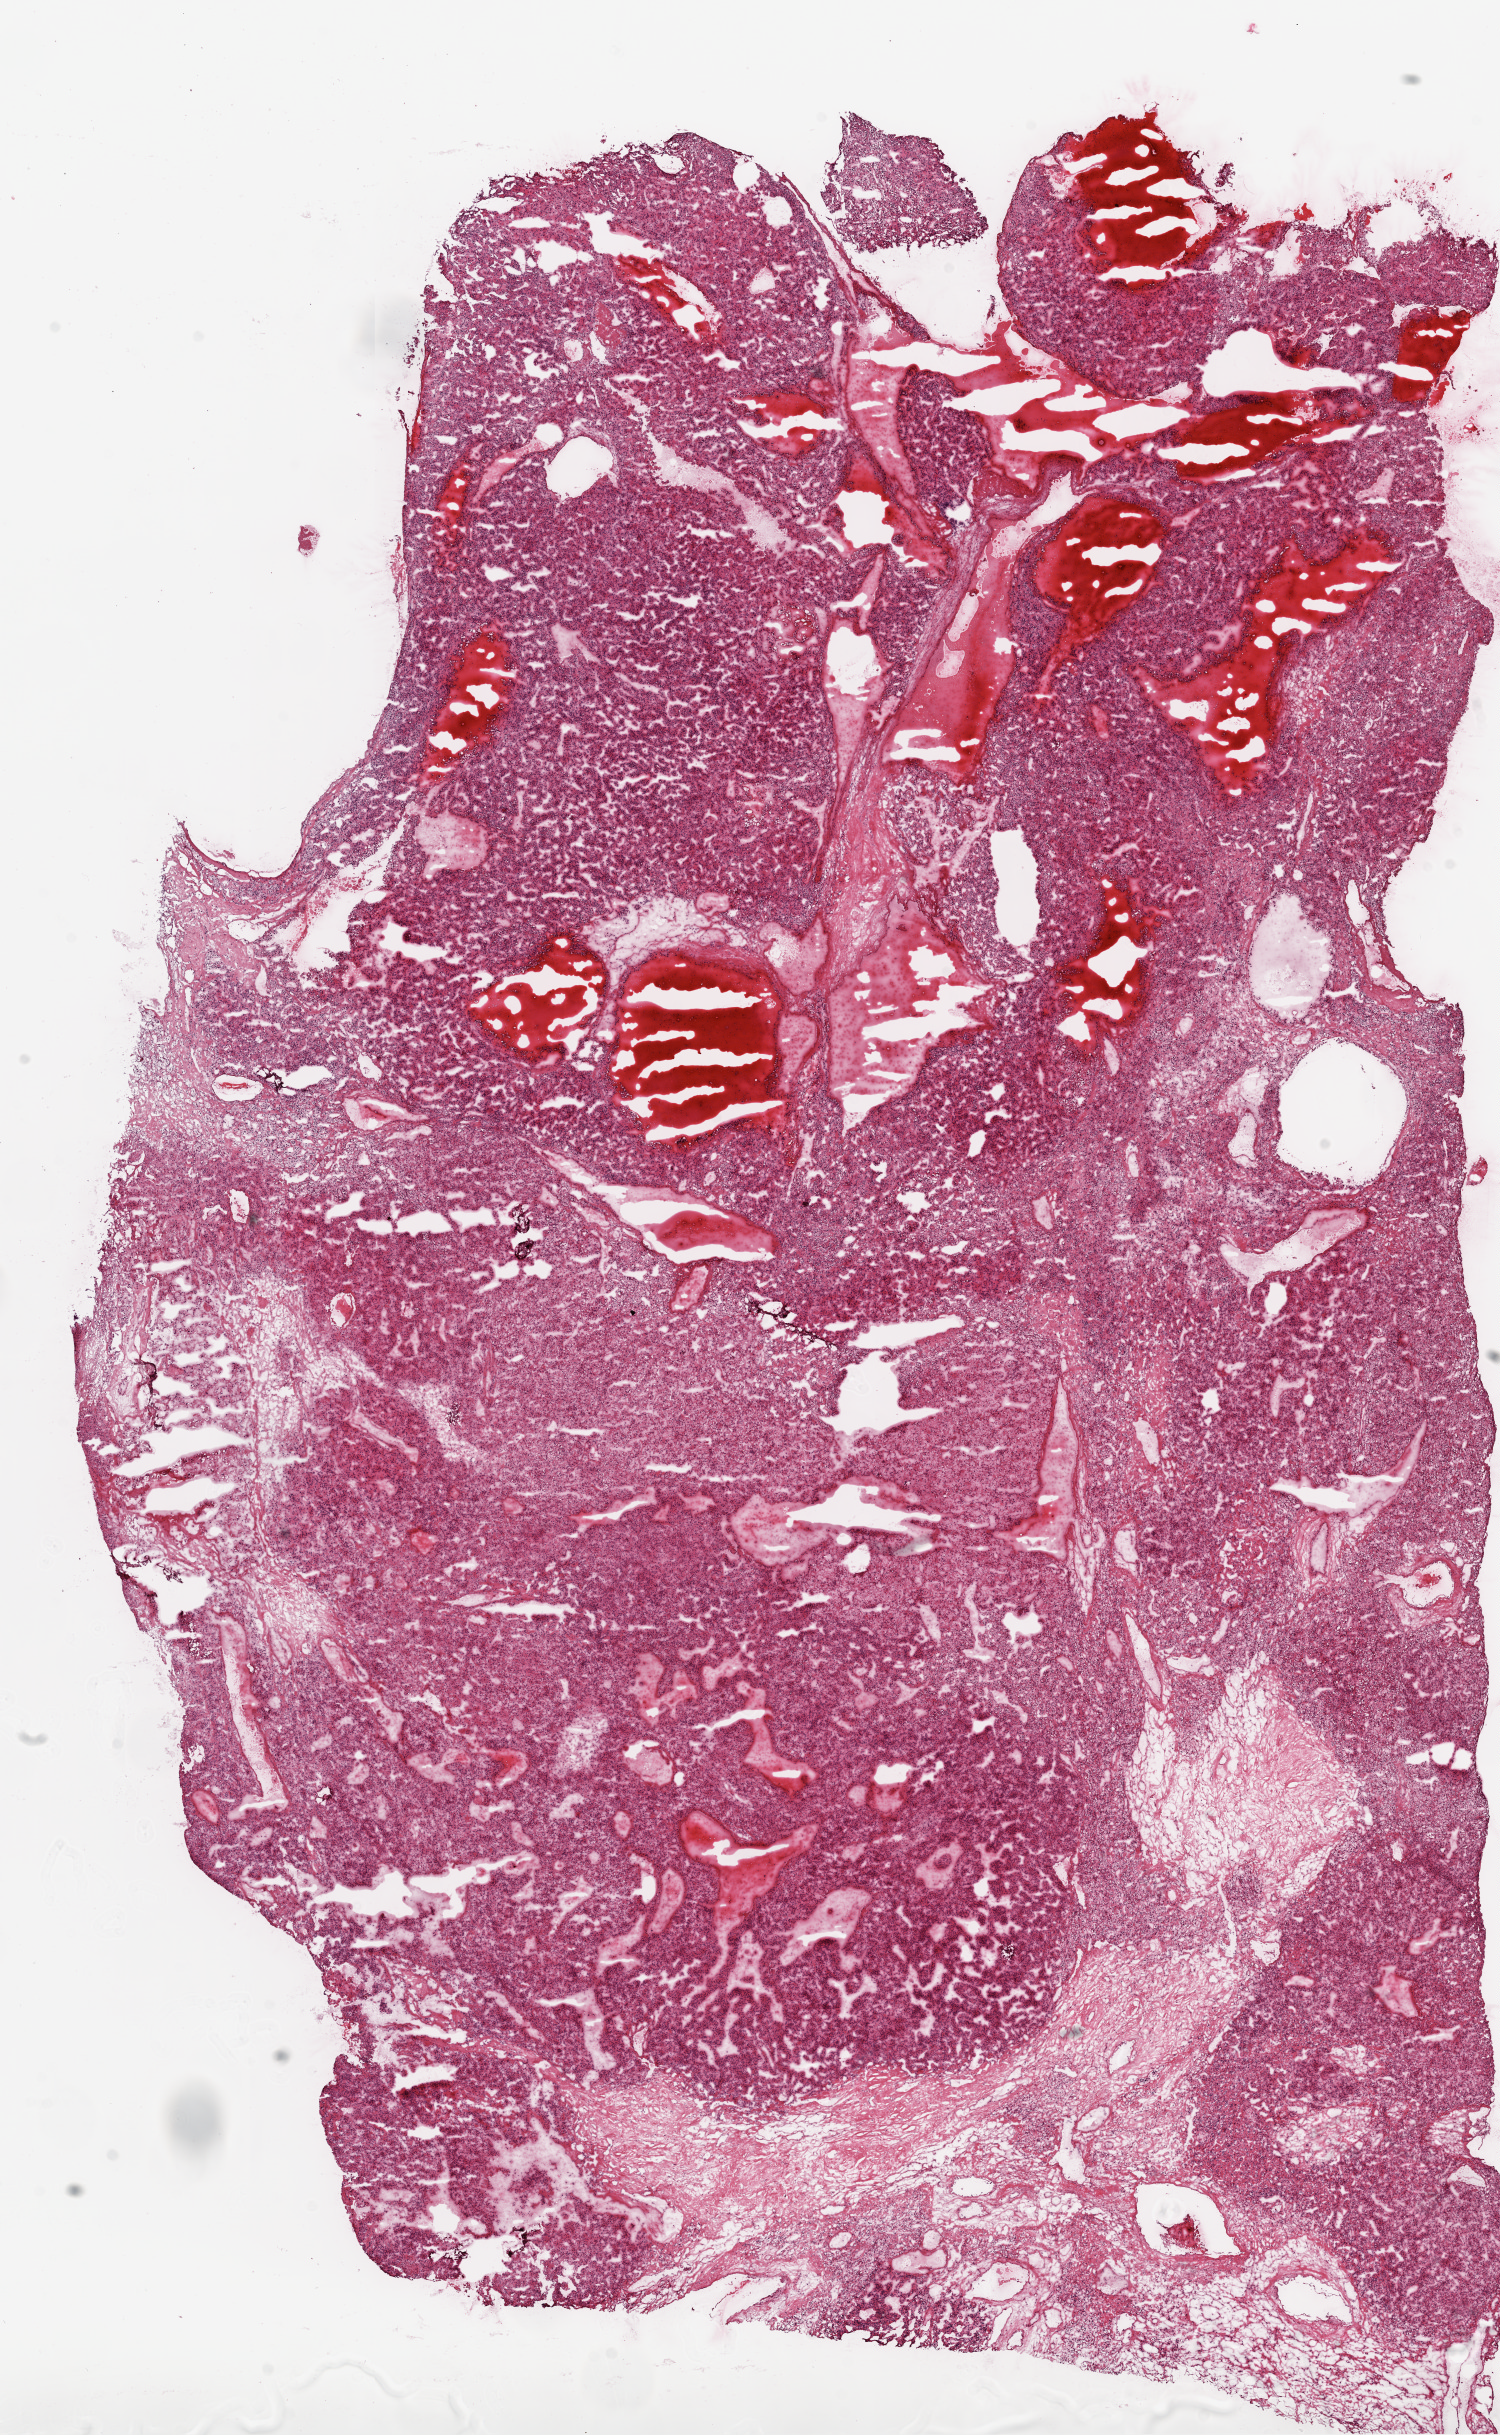
Whole-slide histology image, H&E-stained, low-resolution overview of the scanned area, about 12.0 x 19.5 mm (slide scanned at 20x); frozen section; kidney, primary tumour sample. Patient: male, age at initial diagnosis 63 years. Histologic grade: G4 (undifferentiated). Slide review estimates, as recorded: tumour cells 90%, tumour nuclei 90%, normal cells 0%, stromal cells 10%, necrosis 0%.
* pathologic diagnosis: Clear cell adenocarcinoma, NOS
* lymph nodes positive (case pathology): 0 of 4 examined
* AJCC pathologic stage: IV